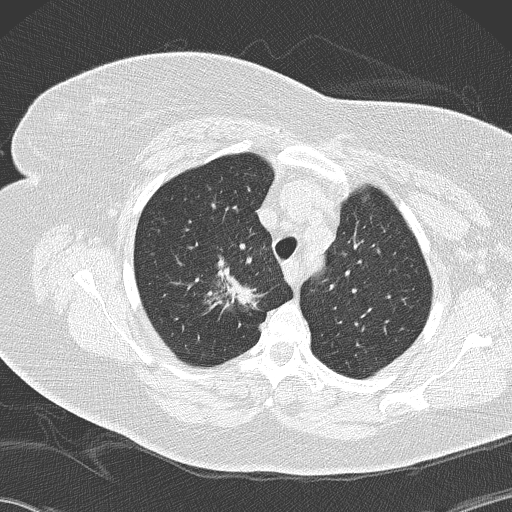
Chest CT (low-dose screening protocol), one axial image, second screening round (one year after baseline), lung window (W 1500 / L -600 HU), 2 mm slice thickness, lung (sharp) reconstruction kernel (B50f), 120 kVp, slice 32 of 146 in the series. Female, age 72 years at enrolment. Former smoker at enrolment.
• Expert reader's lesion annotation, bounding box <179,241,263,328> (left, top, right, bottom; pixels).
• The screening reader recorded 4 non-calcified nodules or masses ≥4 mm on this exam (right lower lobe, right lower lobe, right lower lobe, right upper lobe); which of them this box marks is not recorded.
• Official screen result: positive, other.